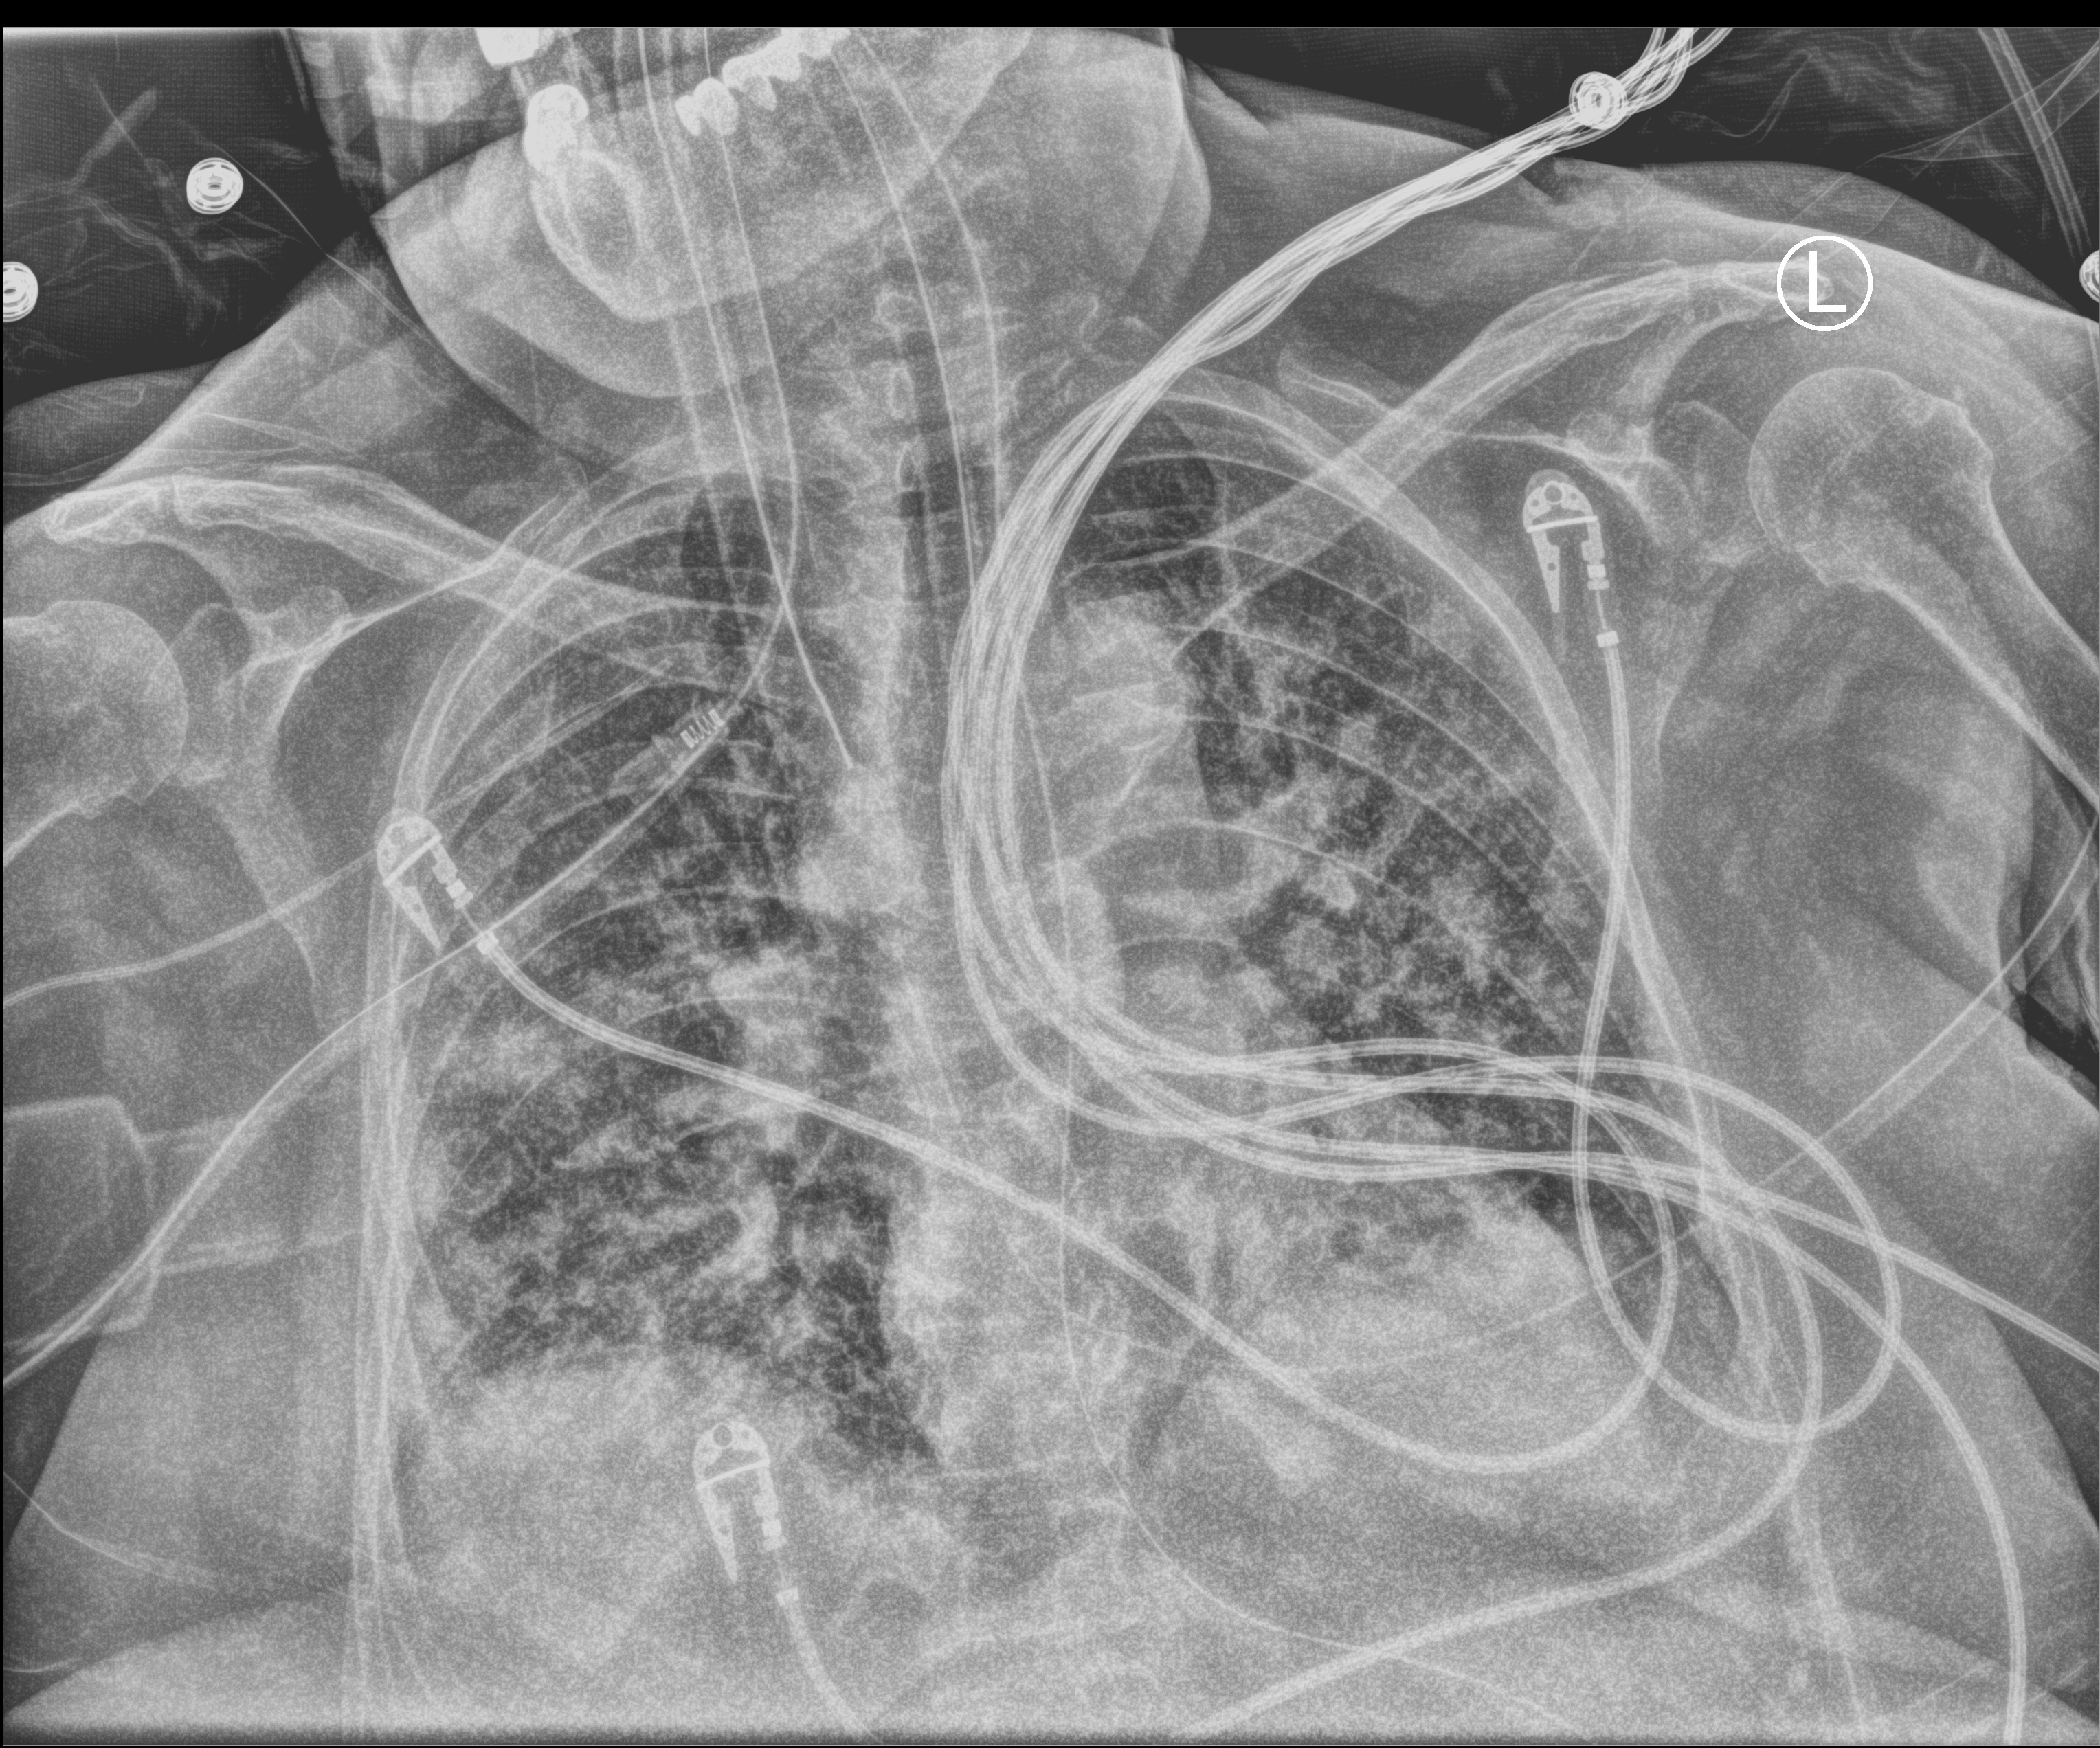
Bedside chest radiograph (computed radiography); anteroposterior (AP) projection. Female patient hospitalised with COVID-19, age 60–74 years.
Admission-level facts for this patient (not findings on this image; timing relative to this image not recorded): admitted to intensive care during this hospital stay: yes; COPD (admission record): no.